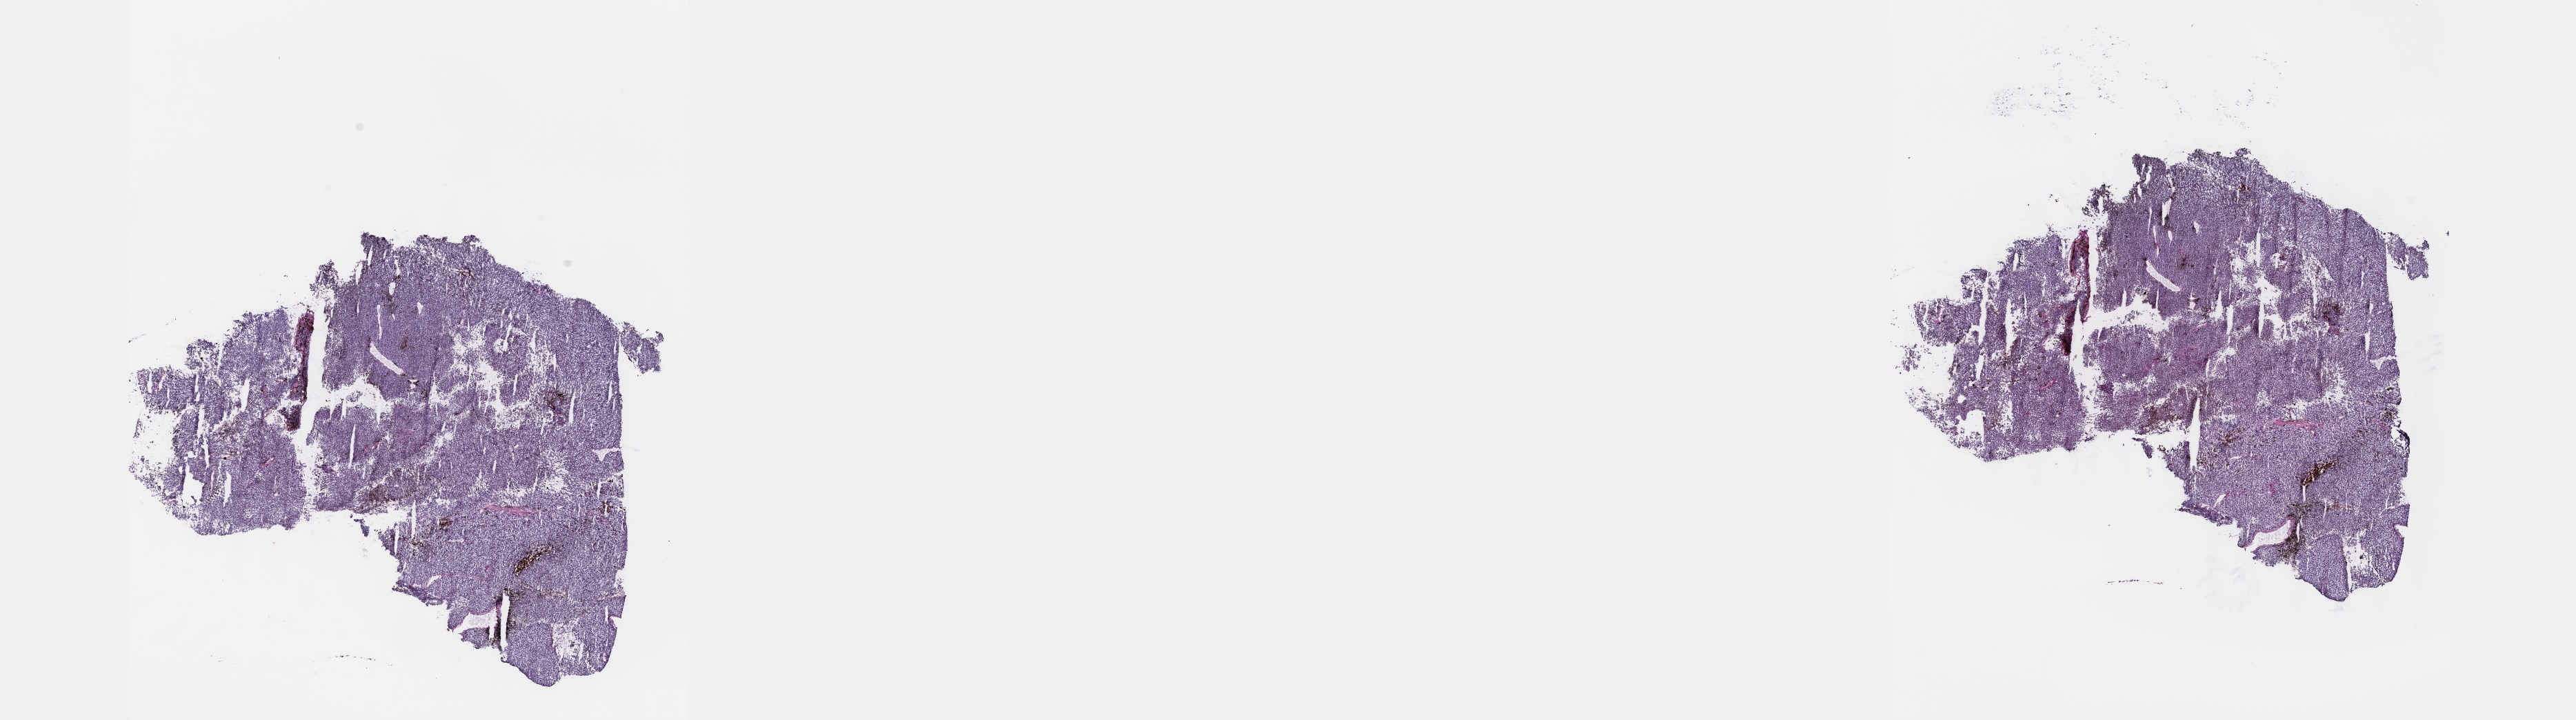
H&E whole-slide image — a low-resolution overview of the entire scanned area, about 30.2 x 8.4 mm (slide scanned at 40x), frozen section from the top of the tissue portion, sample: primary tumour, uvea. Patient: male, age at initial diagnosis 66 years. Slide review estimates, as recorded: tumour cells 100%, tumour nuclei 80%, normal cells 0%, stromal cells 0%, necrosis 0%. Infiltration values recorded for this section: lymphocyte infiltration 2%, monocyte infiltration 0%, neutrophil infiltration 0%.
AJCC pathologic stage: IIIA (7th edition). Pathologic diagnosis: Spindle cell melanoma, NOS (choroid).